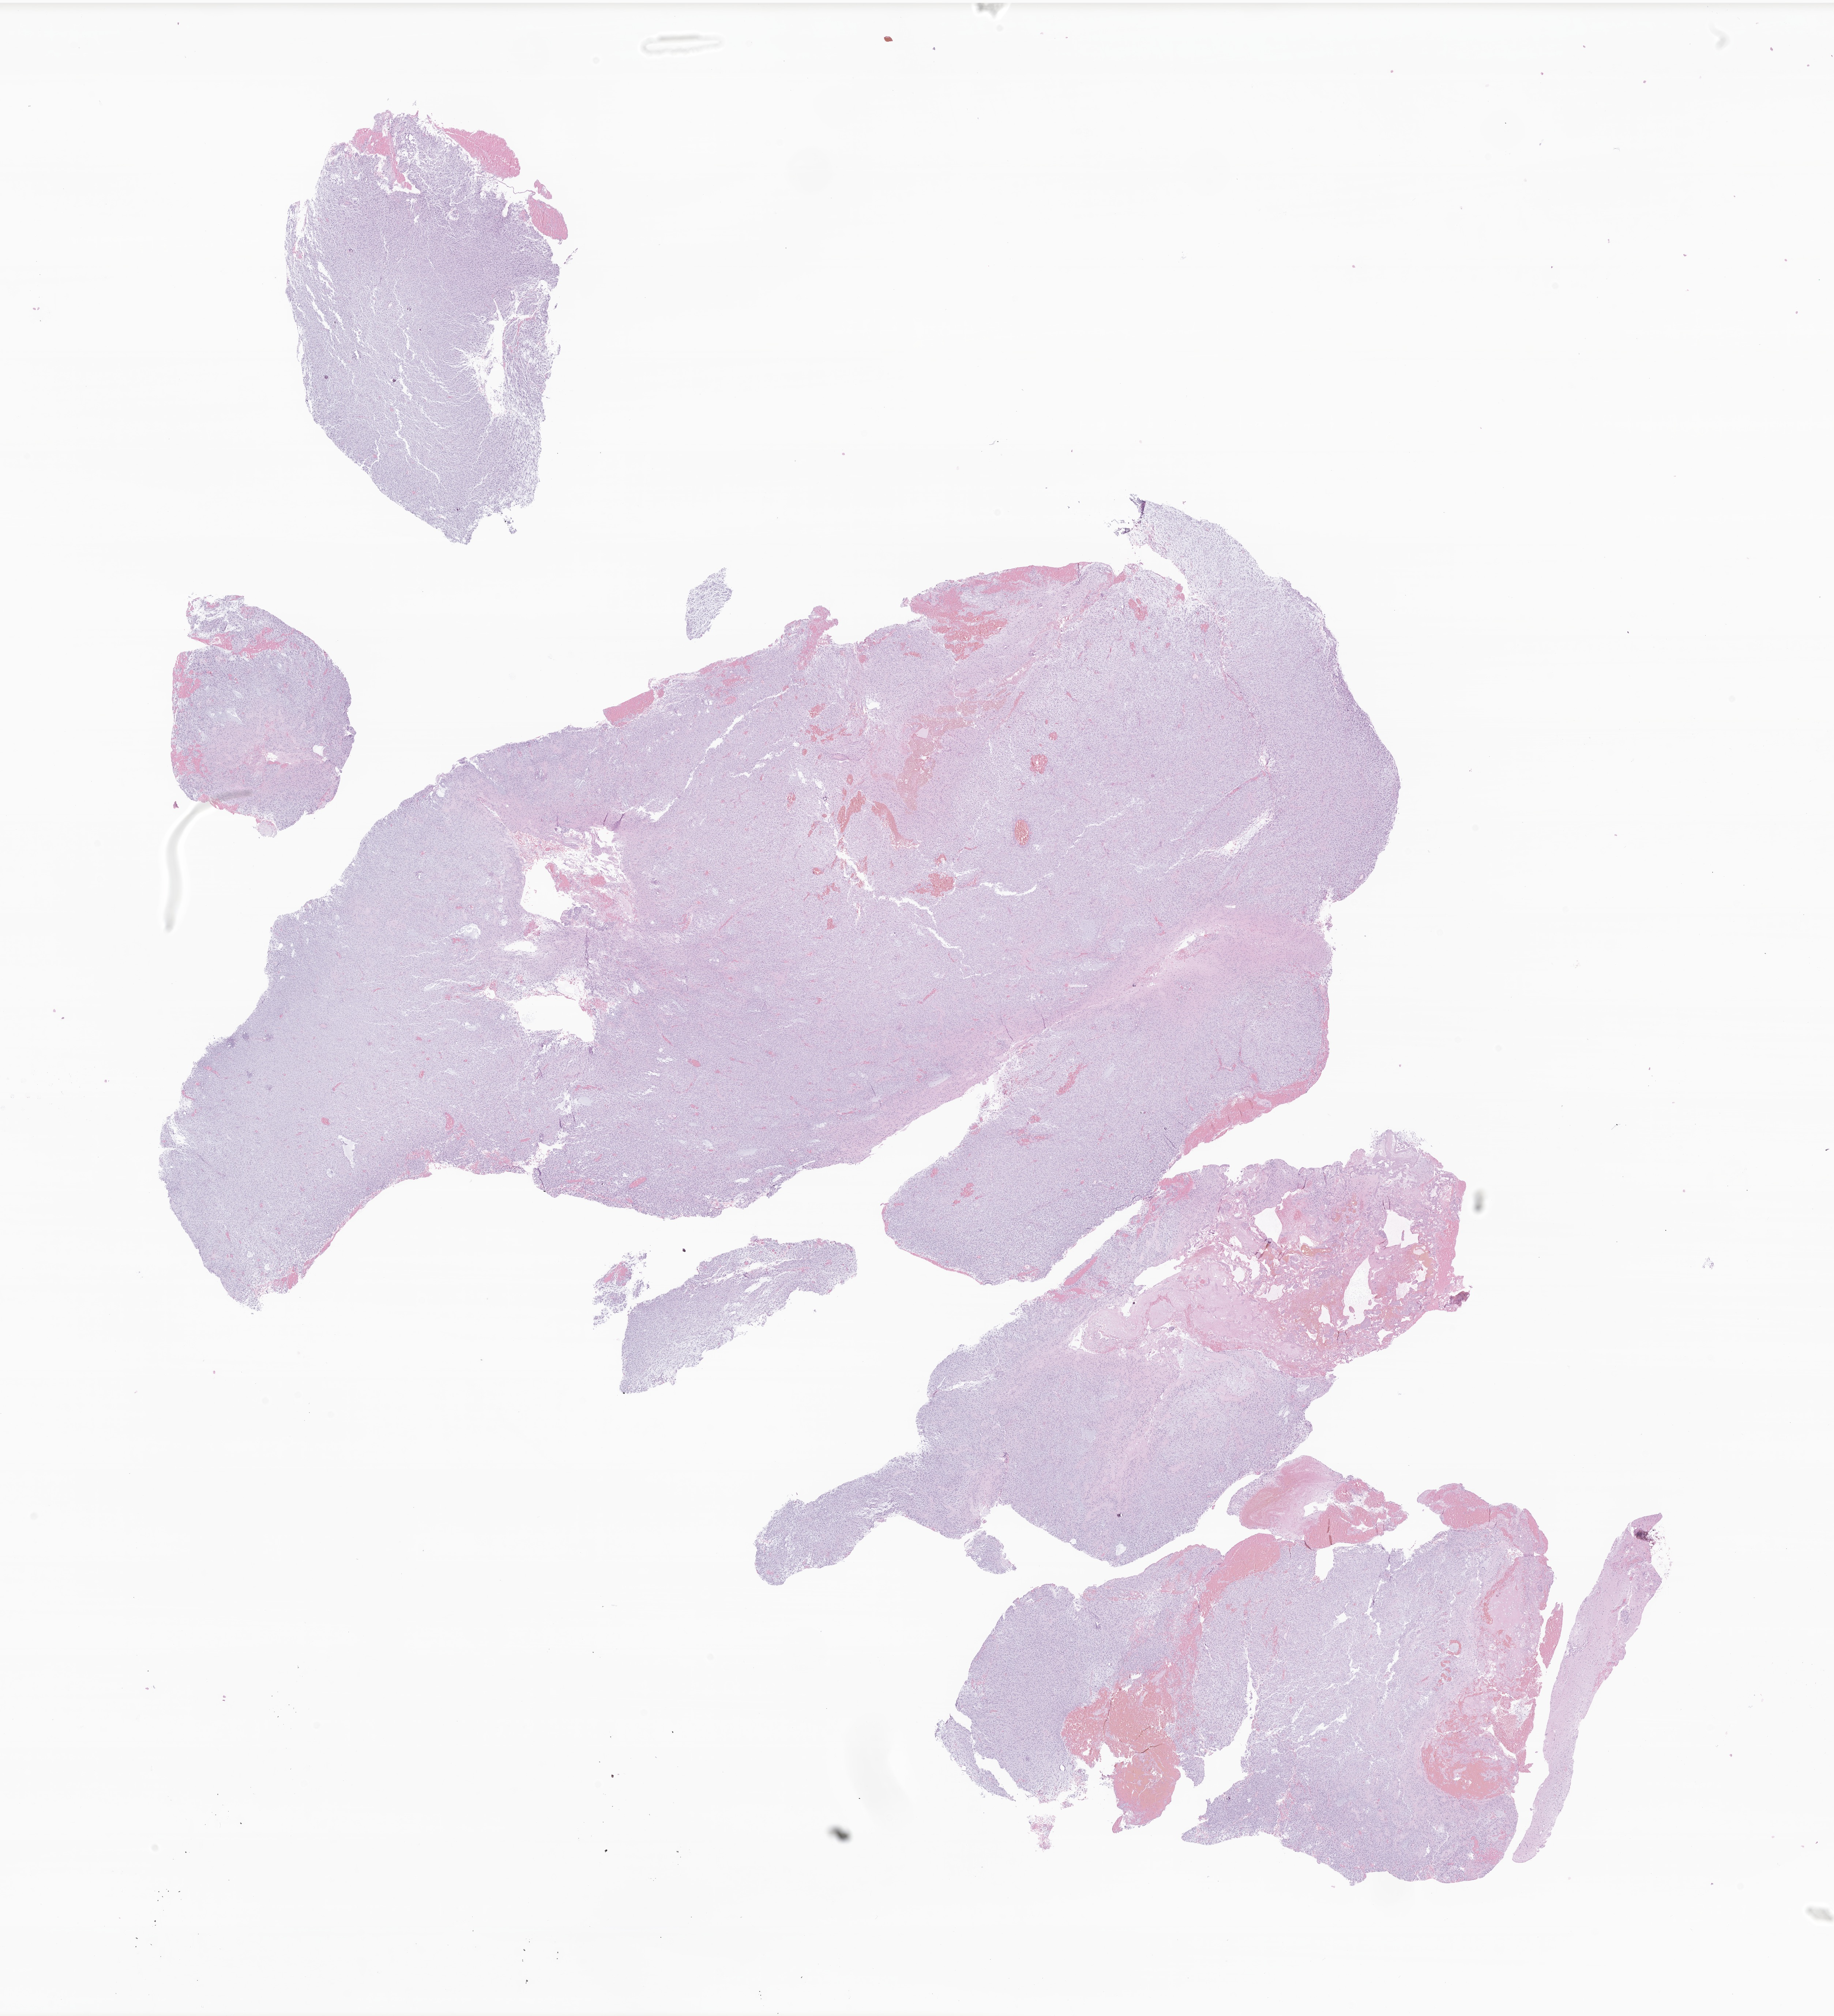
Hematoxylin and eosin (H&E) whole-slide image of tumor tissue from the cerebellum — a low-resolution overview of the entire scanned area, about 21.1 x 23.2 mm, FFPE section. Patient: male, age 58 months (4 years 10 months).
Diagnosis (ICD-O-3 morphology term): Pilocytic astrocytoma.